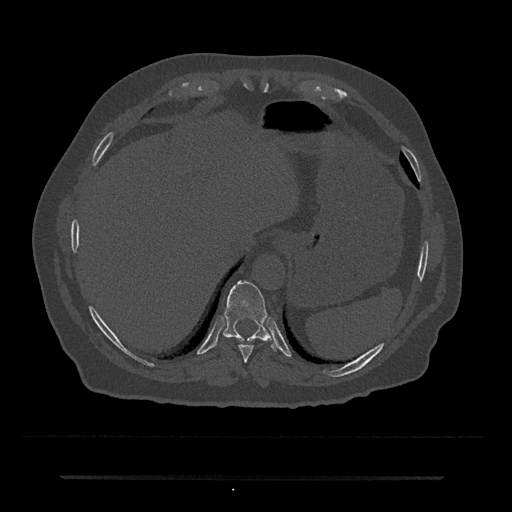
CT including the spine, one axial slice. Position 246 of 797 along the scan axis. Reconstruction kernel Br40s/3. Bone window (W 1800 / L 400 HU). 0.5 mm slice thickness. 512 × 512 image matrix, field of view 437 × 437 mm. Male patient, age 69 years. Case-level facts recorded for this patient, not image findings: primary cancer: prostate.
Structures marked on this image (semi-automatically segmented with operator editing):
- T10 vertebra: bounding box (x1, y1, x2, y2) in pixels: (223, 281, 276, 351)
- T9 vertebra: (238, 344, 254, 363)